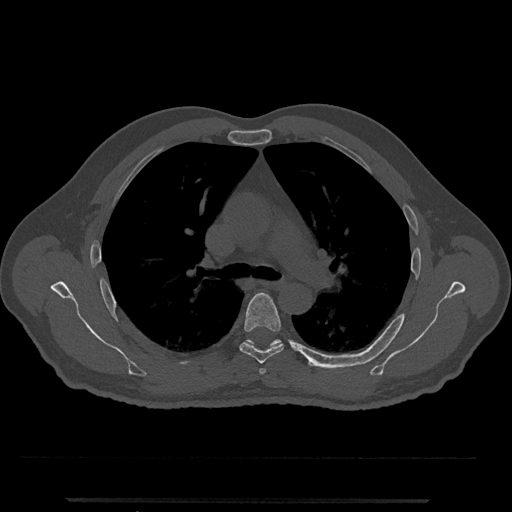
CT including the spine, one axial slice. Slice 784 of 797 in the series (ordered by position). Reconstruction kernel Br40s/3. Bone window (W 1800 / L 400 HU). 512 × 512 image matrix, field of view 419 × 419 mm. Patient: male, 63 years. Case-level facts recorded for this patient, not image findings: primary cancer: prostate.
Structures marked on this image (semi-automatic segmentation, software-assisted and operator-edited):
- T5 vertebra: bounding box <239,293,284,364> (left, top, right, bottom; pixels)
- T6 vertebra: <245,339,281,347>